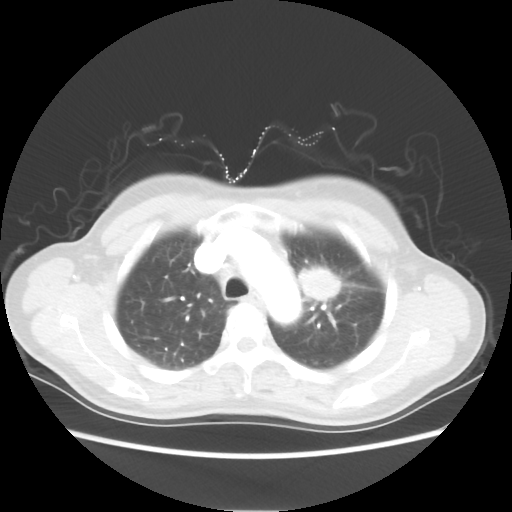
Chest CT, one axial slice; slice 41 of 54 in the series (ordered by position); reconstruction kernel STANDARD; 80 kVp; lung window (W 1500 / L -600 HU); 5 mm slice thickness; 512 × 512 image matrix, field of view 360 × 360 mm. Patient: female, 53 years. From the clinical record (not read from this slice): clinical TNM (as recorded): T1c N0 M0.
Outlined on this slice (rectangle marked by the reading radiologist):
- lung tumour (recorded histology: adenocarcinoma): bounding box <296,257,353,306> (left, top, right, bottom; pixels)
- lung tumour (recorded histology: adenocarcinoma): <297,259,348,302>